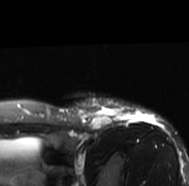
MRI of an extremity soft-tissue mass, one axial slice. Slice 59 of 77 in the series (ordered by position). T2-weighted fat-saturated. MR volume resampled by the dataset authors to the PET/CT grid (not the native acquisition matrix). 189 × 186 image matrix. Female patient. Case-level facts recorded for this patient, not image findings: histological type: leiomyosarcoma; grade: high; site of the primary tumour: groin.
Structures marked on this image (expert contour drawn on MRI and transferred to this co-registered scan by the dataset authors):
- gross tumour volume including surrounding oedema: bounding box [x1, y1, x2, y2] px = [58, 97, 162, 130]
- gross tumour volume (mass): [86, 111, 112, 130]